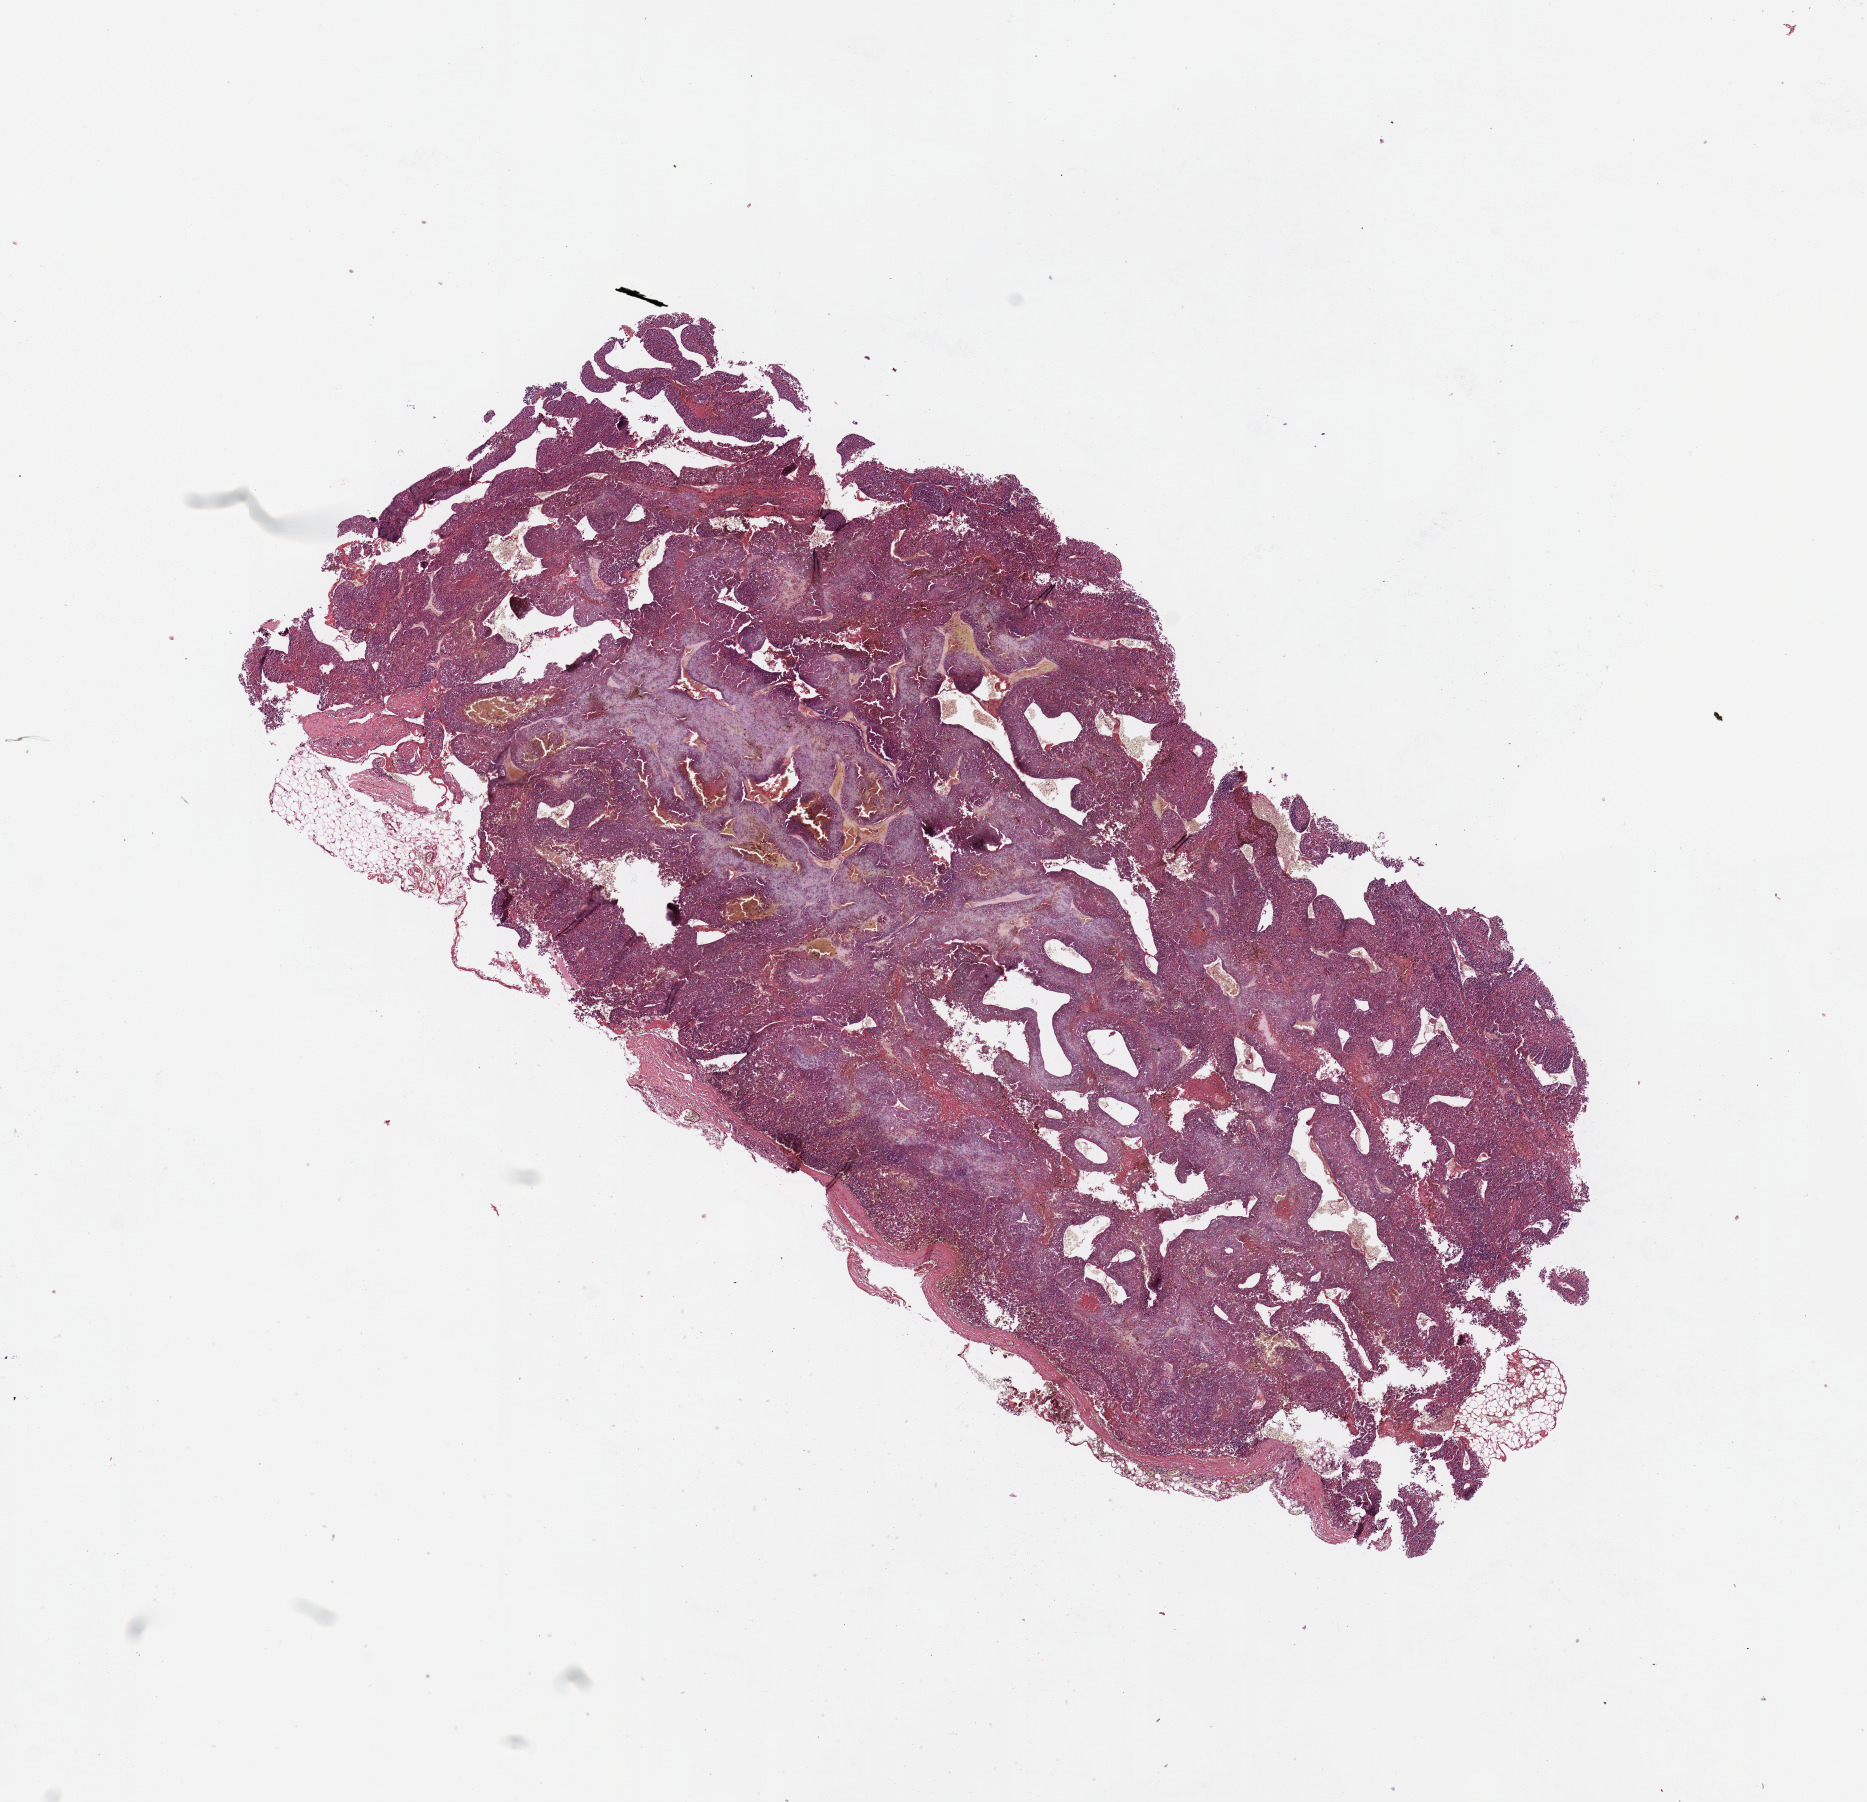
Whole-slide histology image, H&E — whole scanned area (about 14.8 x 14.3 mm, slide scanned at 20x) shown as a low-resolution overview. Melanoma tumour tissue; sampled site not recorded. Male, 60 y/o.
Patient diagnosis (cohort enrolment): cutaneous melanoma (skin). Primary tumour site (as recorded): extremities.